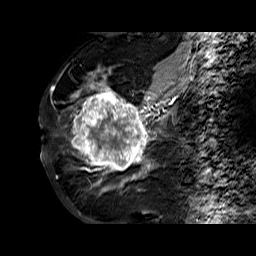
Breast MRI (dynamic contrast-enhanced), one sagittal slice. Slice 31 of 60 in the series (ordered by position). Dynamic contrast-enhanced series, time point 2 of 6 at this slice position (early post-contrast). 1.5 T. TE 6.3 ms, TR 32.4 ms. 4 mm slice thickness. 256 × 256 image matrix. Female patient. From the clinical record (not read from this slice): setting: breast cancer imaged before/during neoadjuvant chemotherapy; receptor status: HR-positive, HER2-negative.
Outlined on this slice (semi-automatic segmentation, software-assisted and operator-edited):
- analysis volume of interest (the breast-tissue region the enhancement analysis was run in; not a lesion): box from (x=68, y=72) to (x=177, y=183) px
- tumour enhancement mask (voxels above the 100 % enhancement threshold inside the analysis volume of interest): (x=73, y=82)–(x=175, y=183)